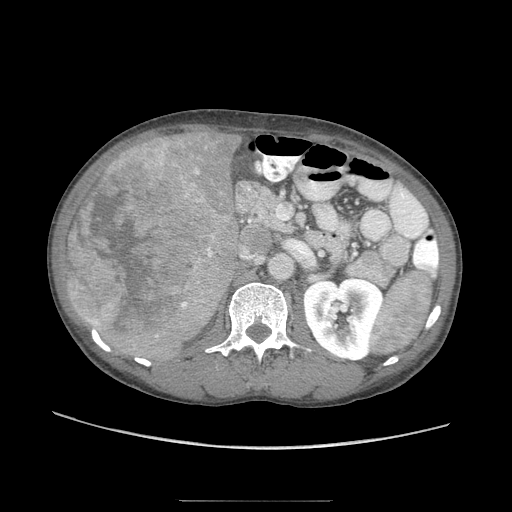
Contrast-enhanced abdominal CT (liver protocol), one axial slice; slice 35 of 103 in the series (ordered by position); reconstruction kernel STANDARD; soft-tissue window (W 400 / L 40 HU); 2.5 mm slice thickness; 512 × 512 image matrix, field of view 380 × 380 mm. Case-level facts recorded for this patient, not image findings: diagnosis: hepatocellular carcinoma (patient treated with transarterial chemoembolisation; whether this scan precedes or follows treatment is not stated here); TNM stage (as recorded): Stage-IIIA; Child-Pugh class: A; tumour differentiation: moderately differentiated; tumour nodularity: multinodular.
Outlined on this slice (semi-automatically segmented with operator editing):
- liver parenchyma outside the tumour (the mass and vessels are separate outlines, so this box may not span the whole liver): bounding box <68,130,244,353> (left, top, right, bottom; pixels)
- mass: <65,139,220,345>